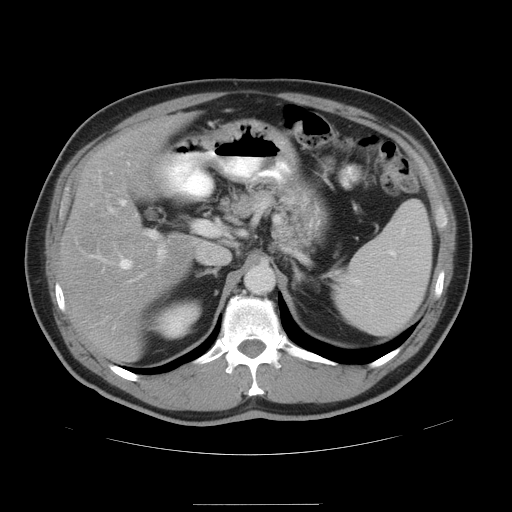
Contrast-enhanced abdominal CT, one axial slice; position 29 of 47 along the scan axis; 120 kVp; intravenous contrast given; soft-tissue window (W 400 / L 40 HU); 5 mm slice thickness; 512 × 512 image matrix, field of view 420 × 420 mm. Male patient, age 61 years. Case-level facts recorded for this patient, not image findings: diagnosis: colorectal cancer liver metastases, imaged before liver resection; multiple liver metastases: no; largest metastasis: 1.2 cm; disease in both lobes: no.
Outlined on this slice (expert manual segmentation):
- hepatic veins: bounding box (x1, y1, x2, y2) in pixels: (98, 199, 132, 268)
- liver: (62, 116, 196, 363)
- planned liver remnant (the part of the liver to remain after resection): (63, 116, 196, 363)
- portal vein (with intrahepatic branches): (110, 208, 217, 262)